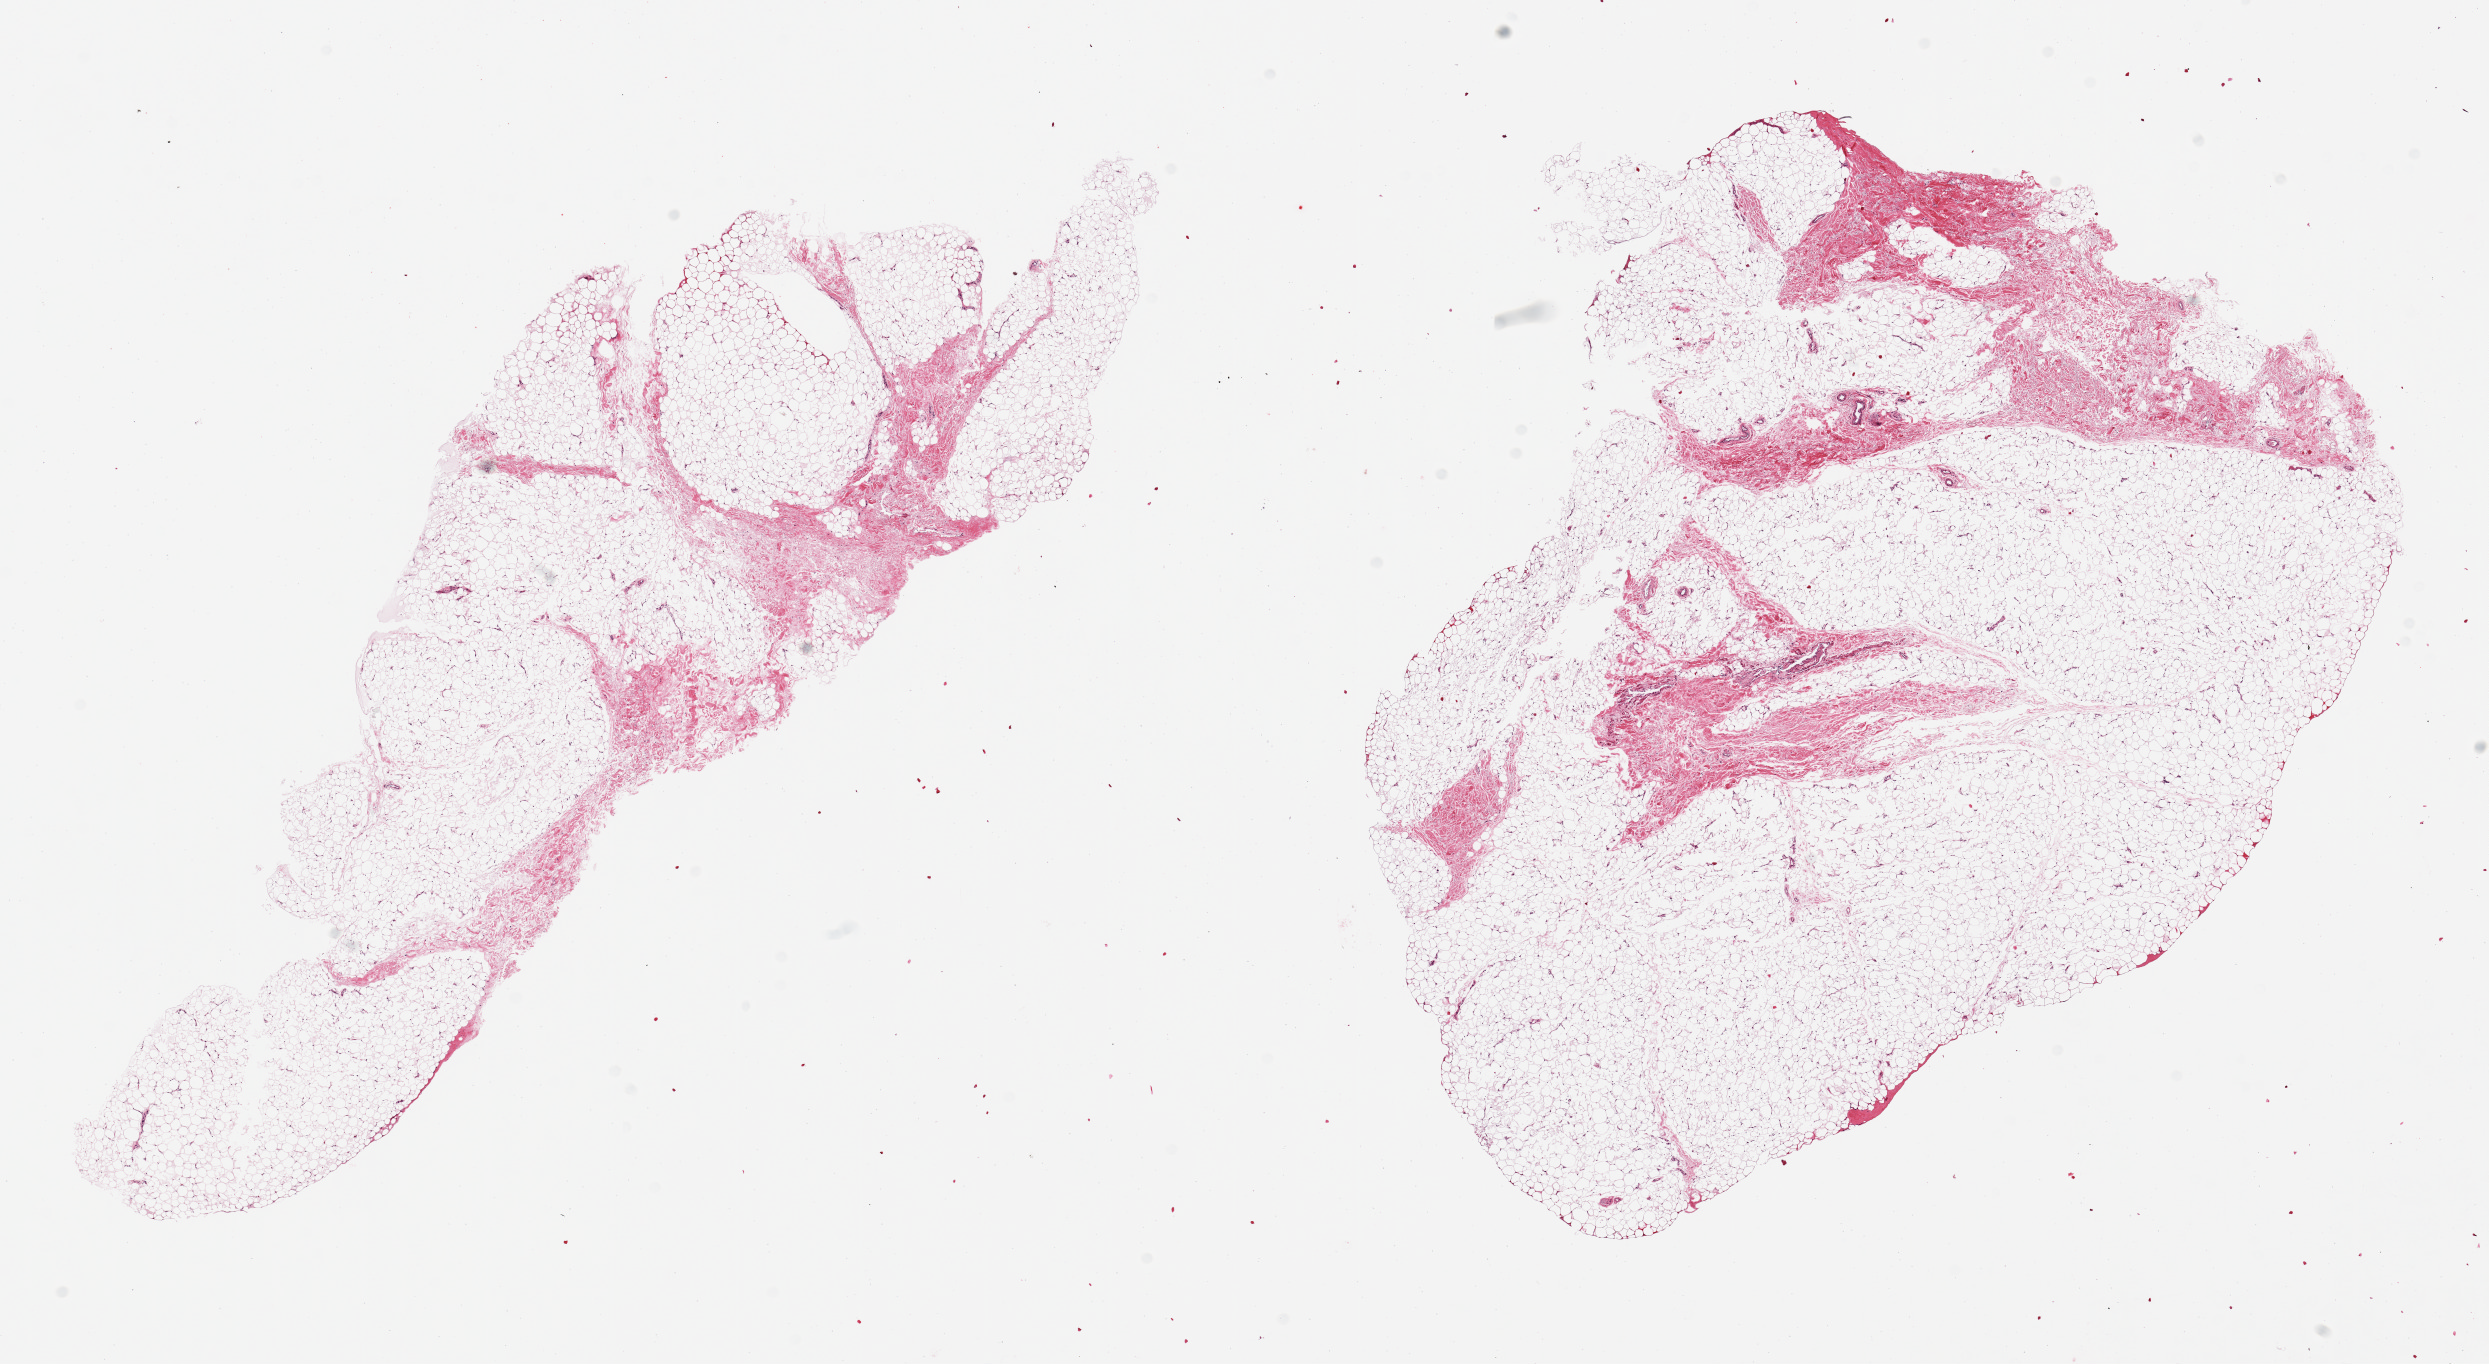
Hematoxylin and eosin (H&E) whole-slide image, brightfield, whole scanned area (about 19.7 x 10.8 mm, slide scanned at 20x) shown as a low-resolution overview; PAXgene-fixed, paraffin-embedded tissue; sampled site (target tissue): adipose tissue; donor tissue sample.
Reviewer comment on this tissue sample: 2 pieces; 20 & 10% fibrous content.